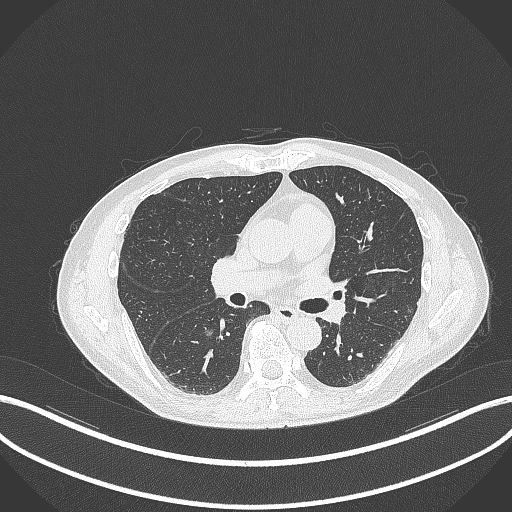
Chest CT, one axial slice. Slice 176 of 323 in the series (ordered by position). 120 kVp. Lung window (W 1500 / L -600 HU). 512 × 512 image matrix, field of view 400 × 400 mm. Patient: male, 61 years. From the clinical record (not read from this slice): clinical TNM (as recorded): T1c N0 M0.
Structures marked on this image (rectangle marked by the reading radiologist):
- lung tumour (recorded histology: adenocarcinoma): box from (x=202, y=326) to (x=218, y=339) px